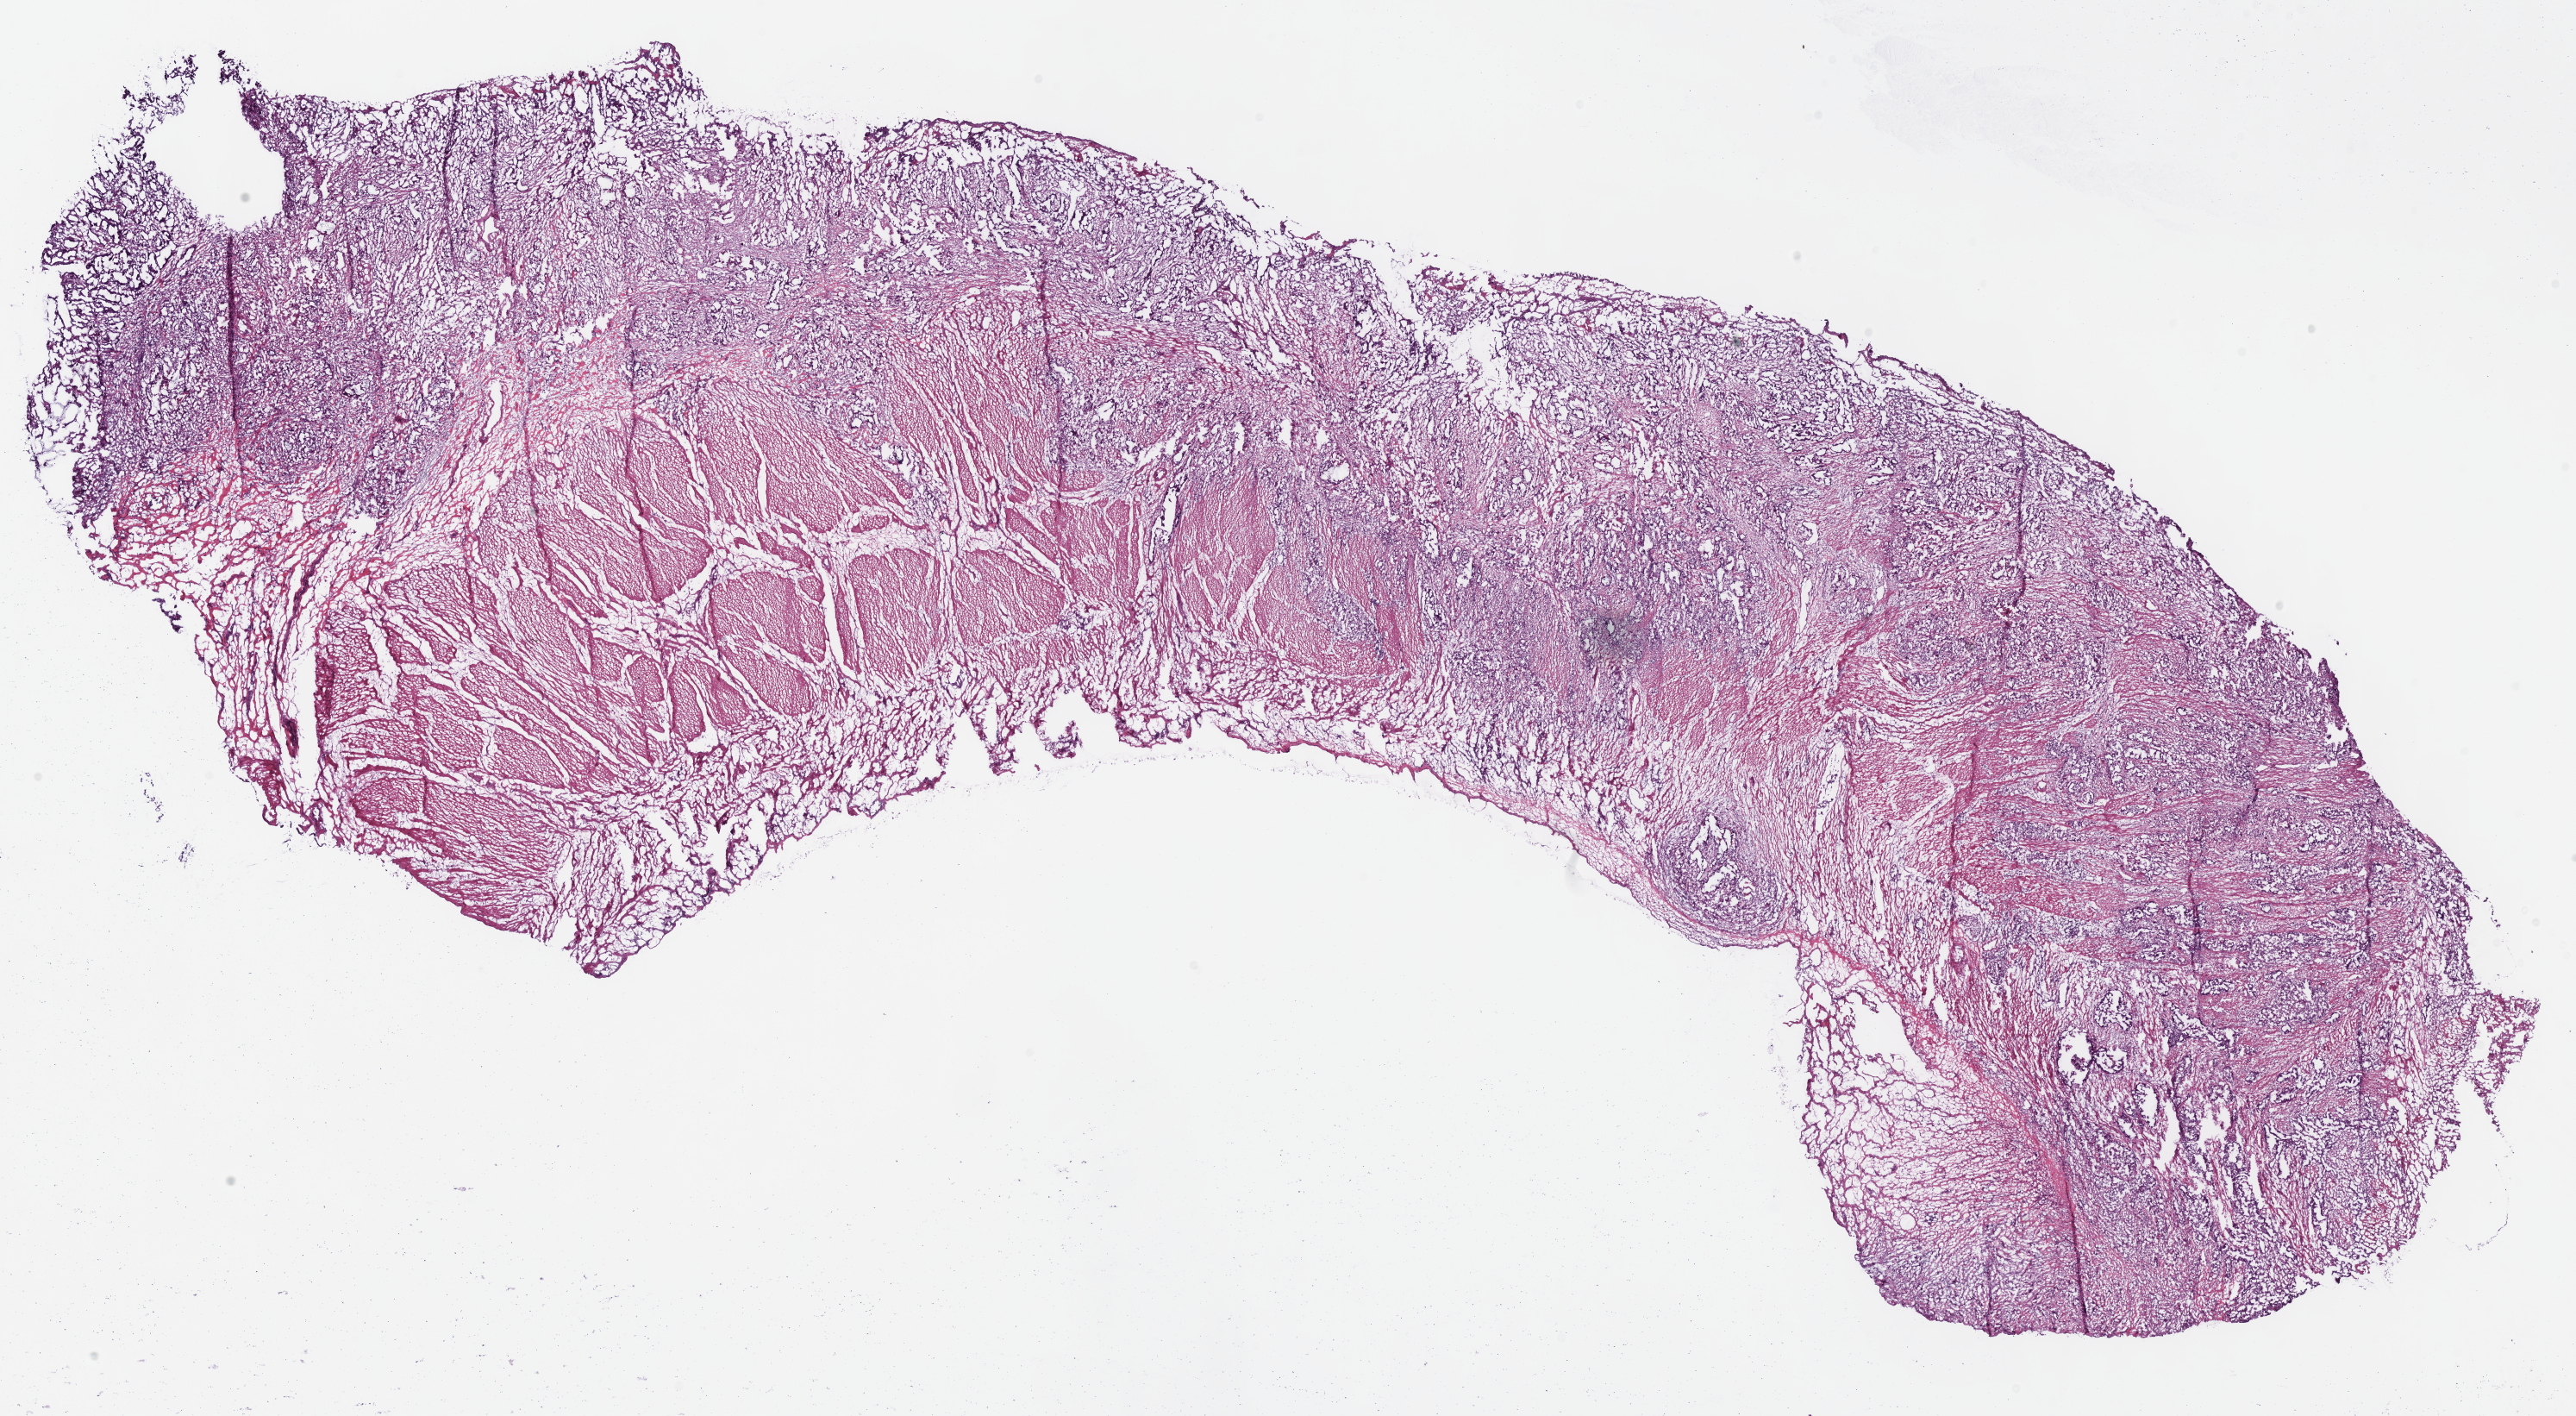
Hematoxylin and eosin (H&E) stained whole-slide image, a low-resolution overview of the entire scanned area, about 23.5 x 12.9 mm, frozen section, primary tumour sample from the stomach. Male, age 72 years at initial diagnosis. Histologic grade: G3 (poorly differentiated). Slide review estimates, as recorded: tumour cells 55%, tumour nuclei 60%, normal cells 25%, stromal cells 18%, necrosis 2%. Infiltration values recorded for this section: lymphocyte infiltration 5%.
TNM: T4 N1 M0. Lymph nodes positive (case pathology): 1 of 7 examined. Pathologic diagnosis: Adenocarcinoma, intestinal type (fundus of stomach). AJCC pathologic stage: III.